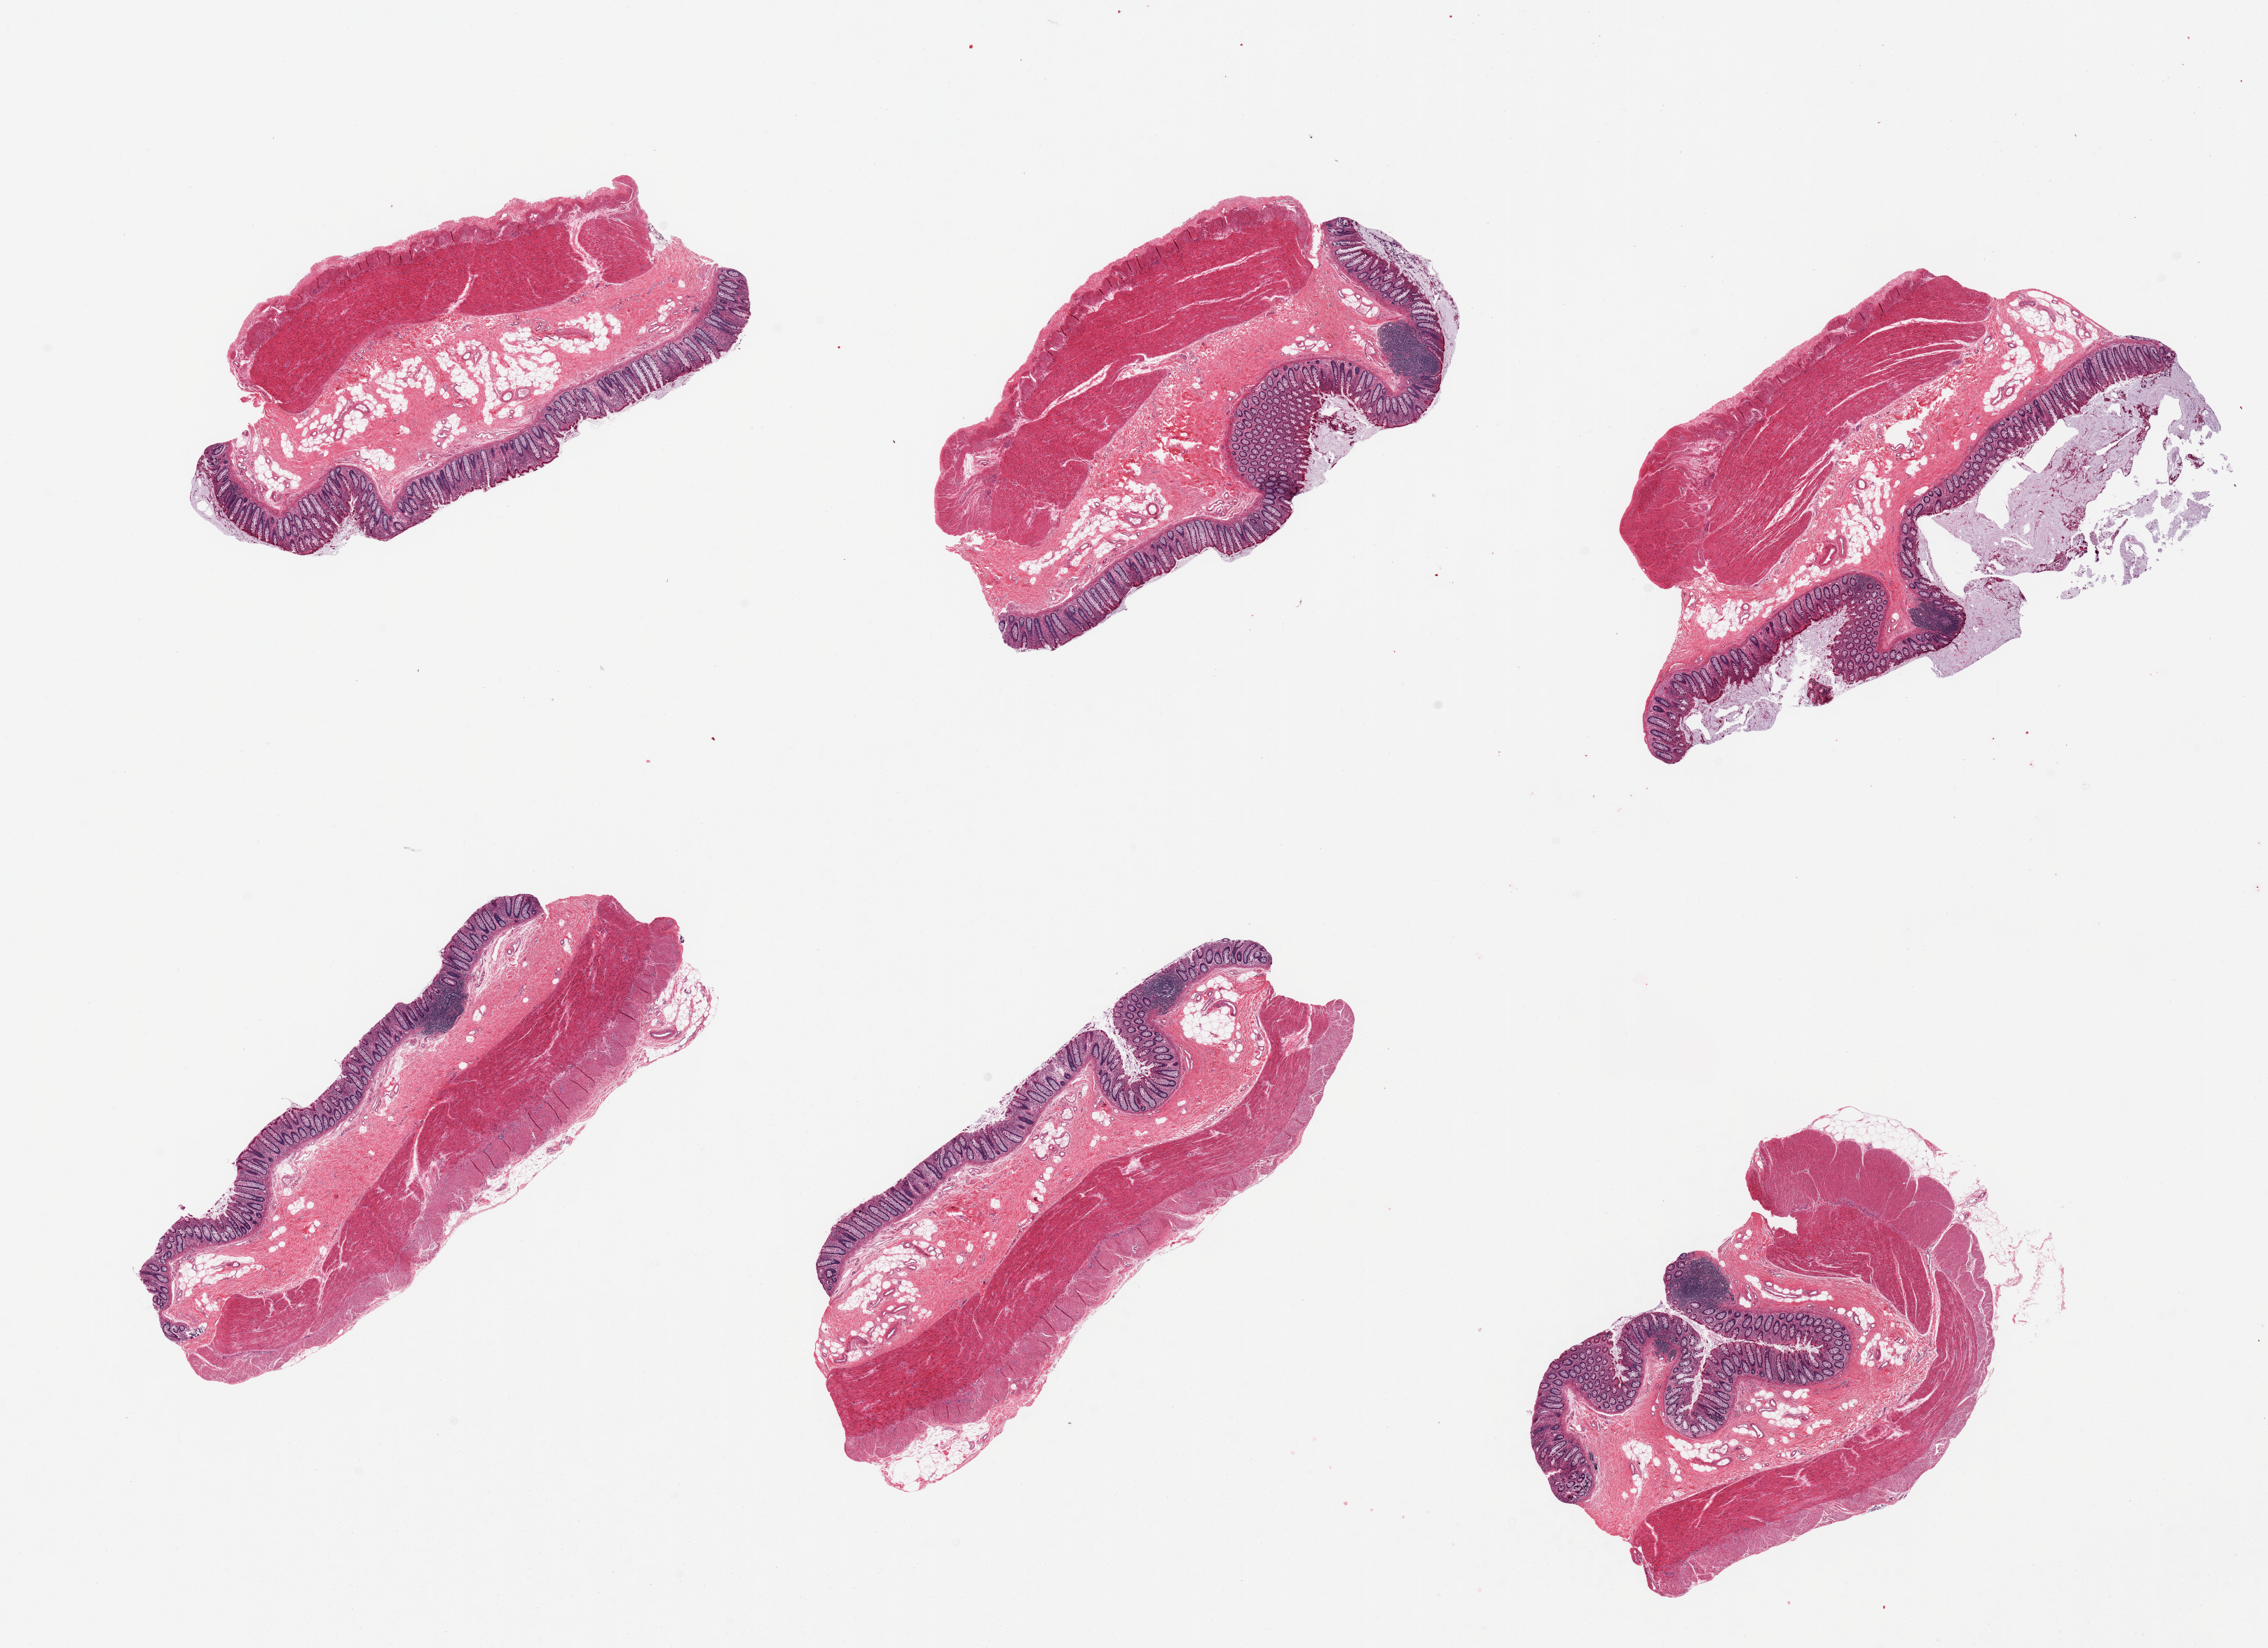
Digitized haematoxylin and eosin-stained section, brightfield, whole scanned area (about 25.6 x 18.6 mm, acquisition: 20x scan) shown as a low-resolution overview. PAXgene-fixed paraffin-embedded (PFPE) section. Sampled site (target tissue): transverse colon. Tissue donor sample. Donor: male.
Reviewer comment on this tissue sample: 6 pieces, well preserved mucosa is ~0.4mm thick, ~15% thickness.